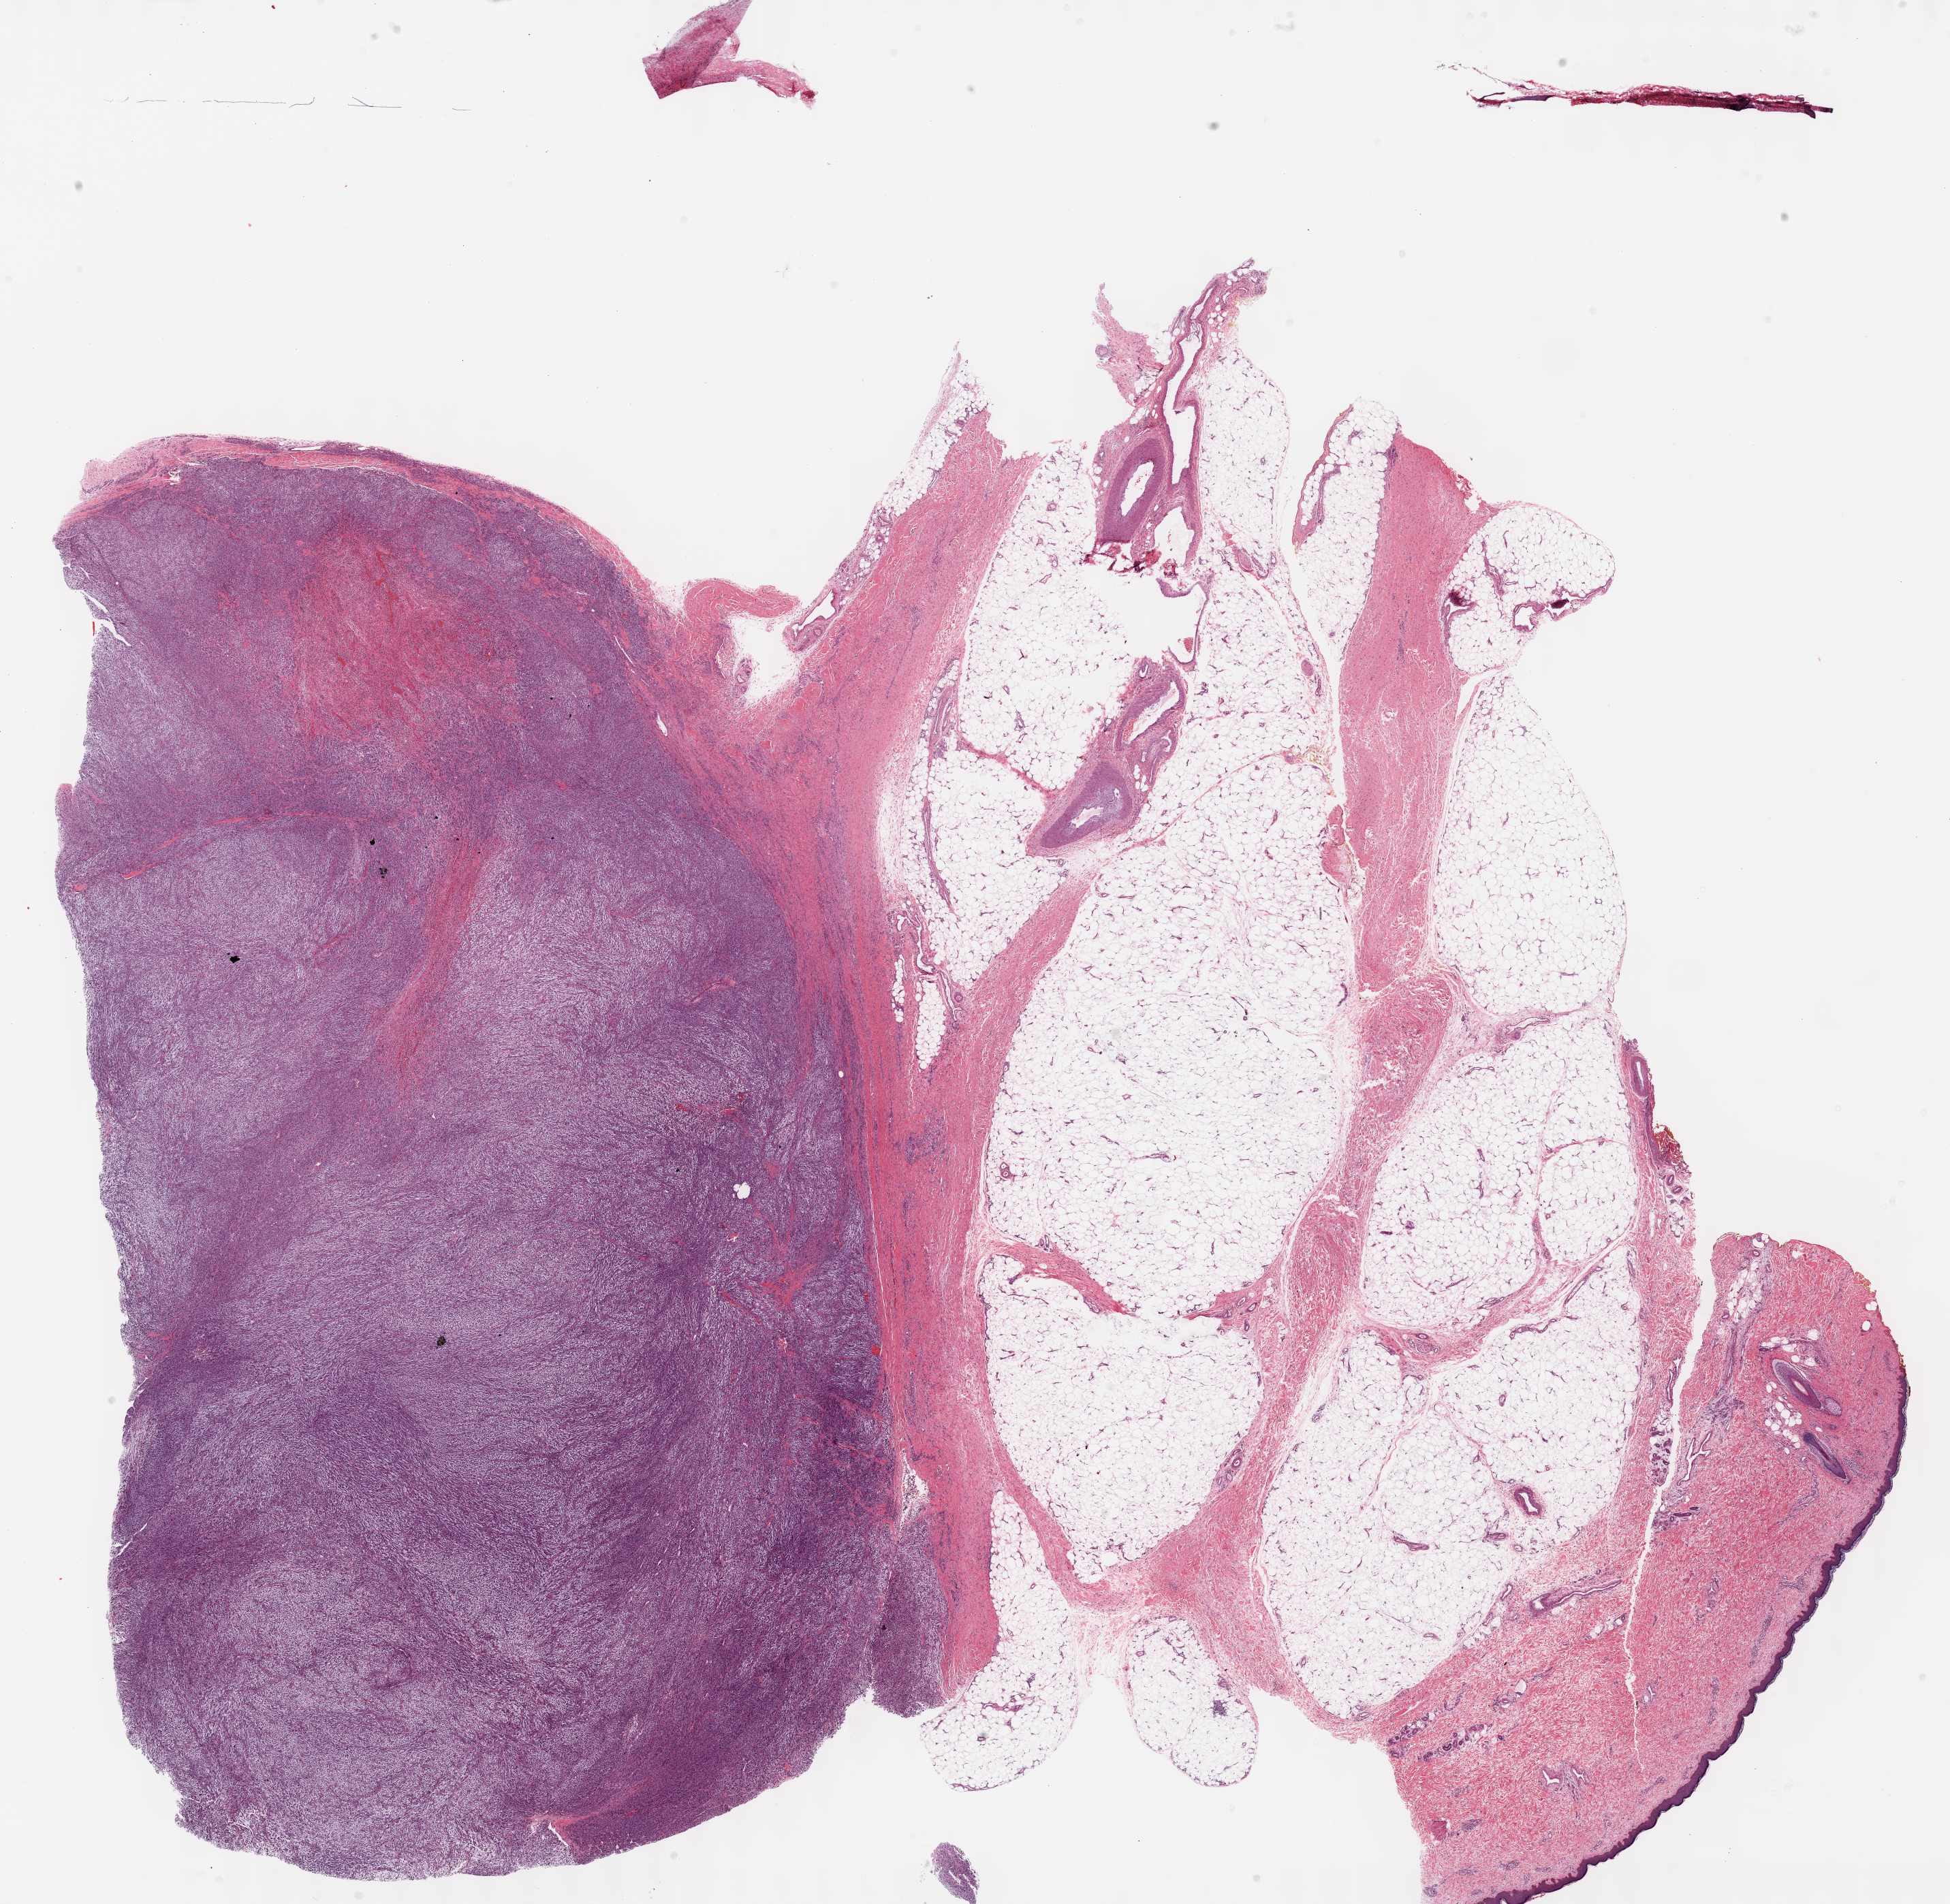
Whole-slide histology image, H&E-stained — whole scanned area (about 23.1 x 22.6 mm, slide scanned at 40x) shown as a low-resolution overview, formalin-fixed paraffin-embedded (FFPE) diagnostic section, sample: primary tumour, connective, subcutaneous and other soft tissues. Patient: female, age at initial diagnosis 68 years.
• diagnosis: Fibromyxosarcoma (connective, subcutaneous and other soft tissues of lower limb and hip)